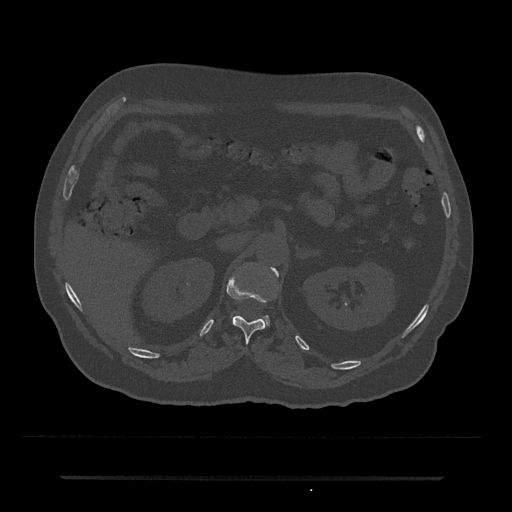
CT including the spine, one axial slice; position 114 of 797 along the scan axis; reconstruction kernel Br40s/3; bone window (W 1800 / L 400 HU); 512 × 512 image matrix, field of view 437 × 437 mm. Patient: male, 69 years. Case-level facts recorded for this patient, not image findings: primary cancer: prostate.
Structures marked on this image (semi-automatically segmented with operator editing):
- L1 vertebra: bounding box [x1, y1, x2, y2] px = [262, 268, 279, 325]
- T12 vertebra: [227, 269, 278, 343]